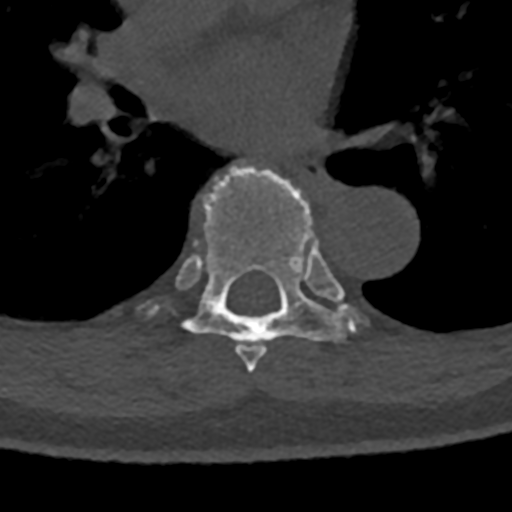
CT including the spine, one axial slice; slice 770 of 797 in the series (ordered by position); reconstruction kernel Br40s/3; 120 kVp; bone window (W 1800 / L 400 HU); 0.5 mm slice thickness; 512 × 512 image matrix. Male patient, age 74 years. From the clinical record (not read from this slice): primary cancer: renal; vertebrae with lytic lesions (as recorded): T10, L1, L2, L3, L4, L5.
Annotated regions visible in this slice (semi-automatically segmented with operator editing):
- T6 vertebra: bounding box [x1, y1, x2, y2] px = [237, 343, 267, 373]
- T7 vertebra: [150, 165, 361, 363]